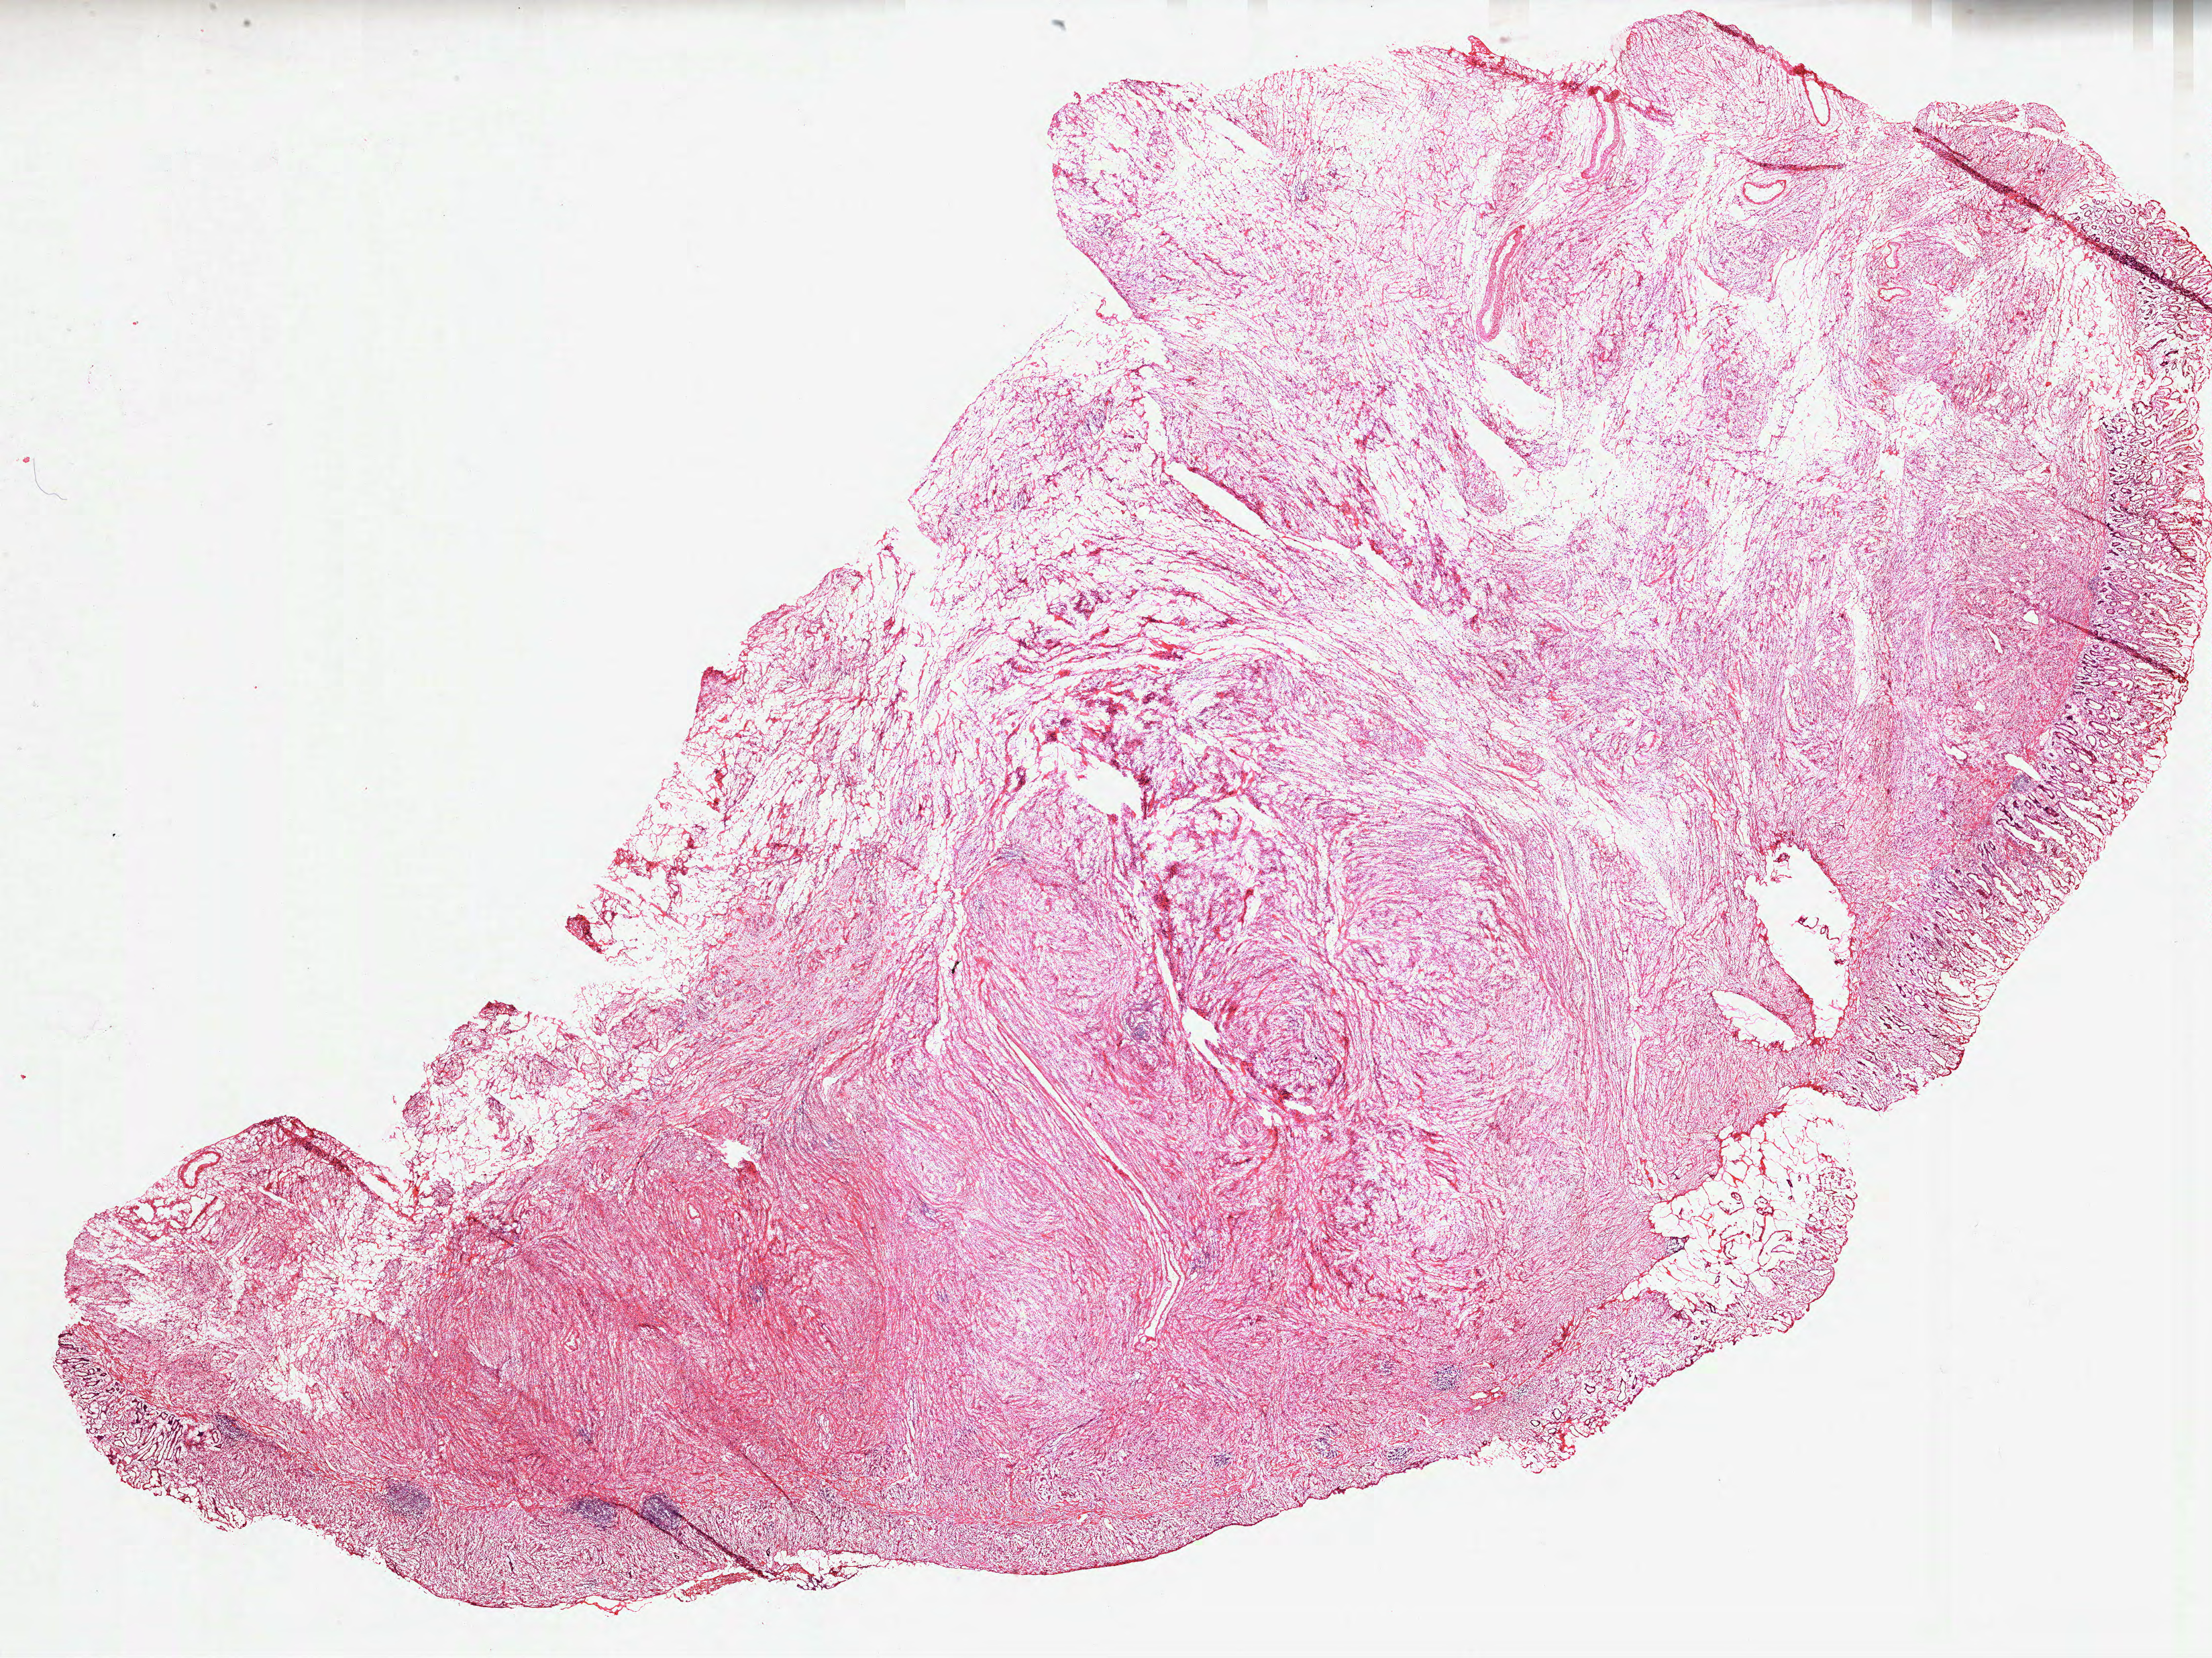
H&E-stained whole-slide image — low-resolution overview of the scanned area, about 26.6 x 19.9 mm (acquisition: 40x scan). Frozen section from the top of the tissue portion. Stomach, primary tumour sample. Patient: male, age at initial diagnosis 61 years. Histologic grade: GX (grade cannot be assessed). Slide review estimates, as recorded: tumour cells 80%, tumour nuclei 75%, normal cells 0%, stromal cells 20%, necrosis 0%.
• diagnosis: Carcinoma, diffuse type (gastric antrum)
• AJCC pathologic stage: IIB (7th edition)